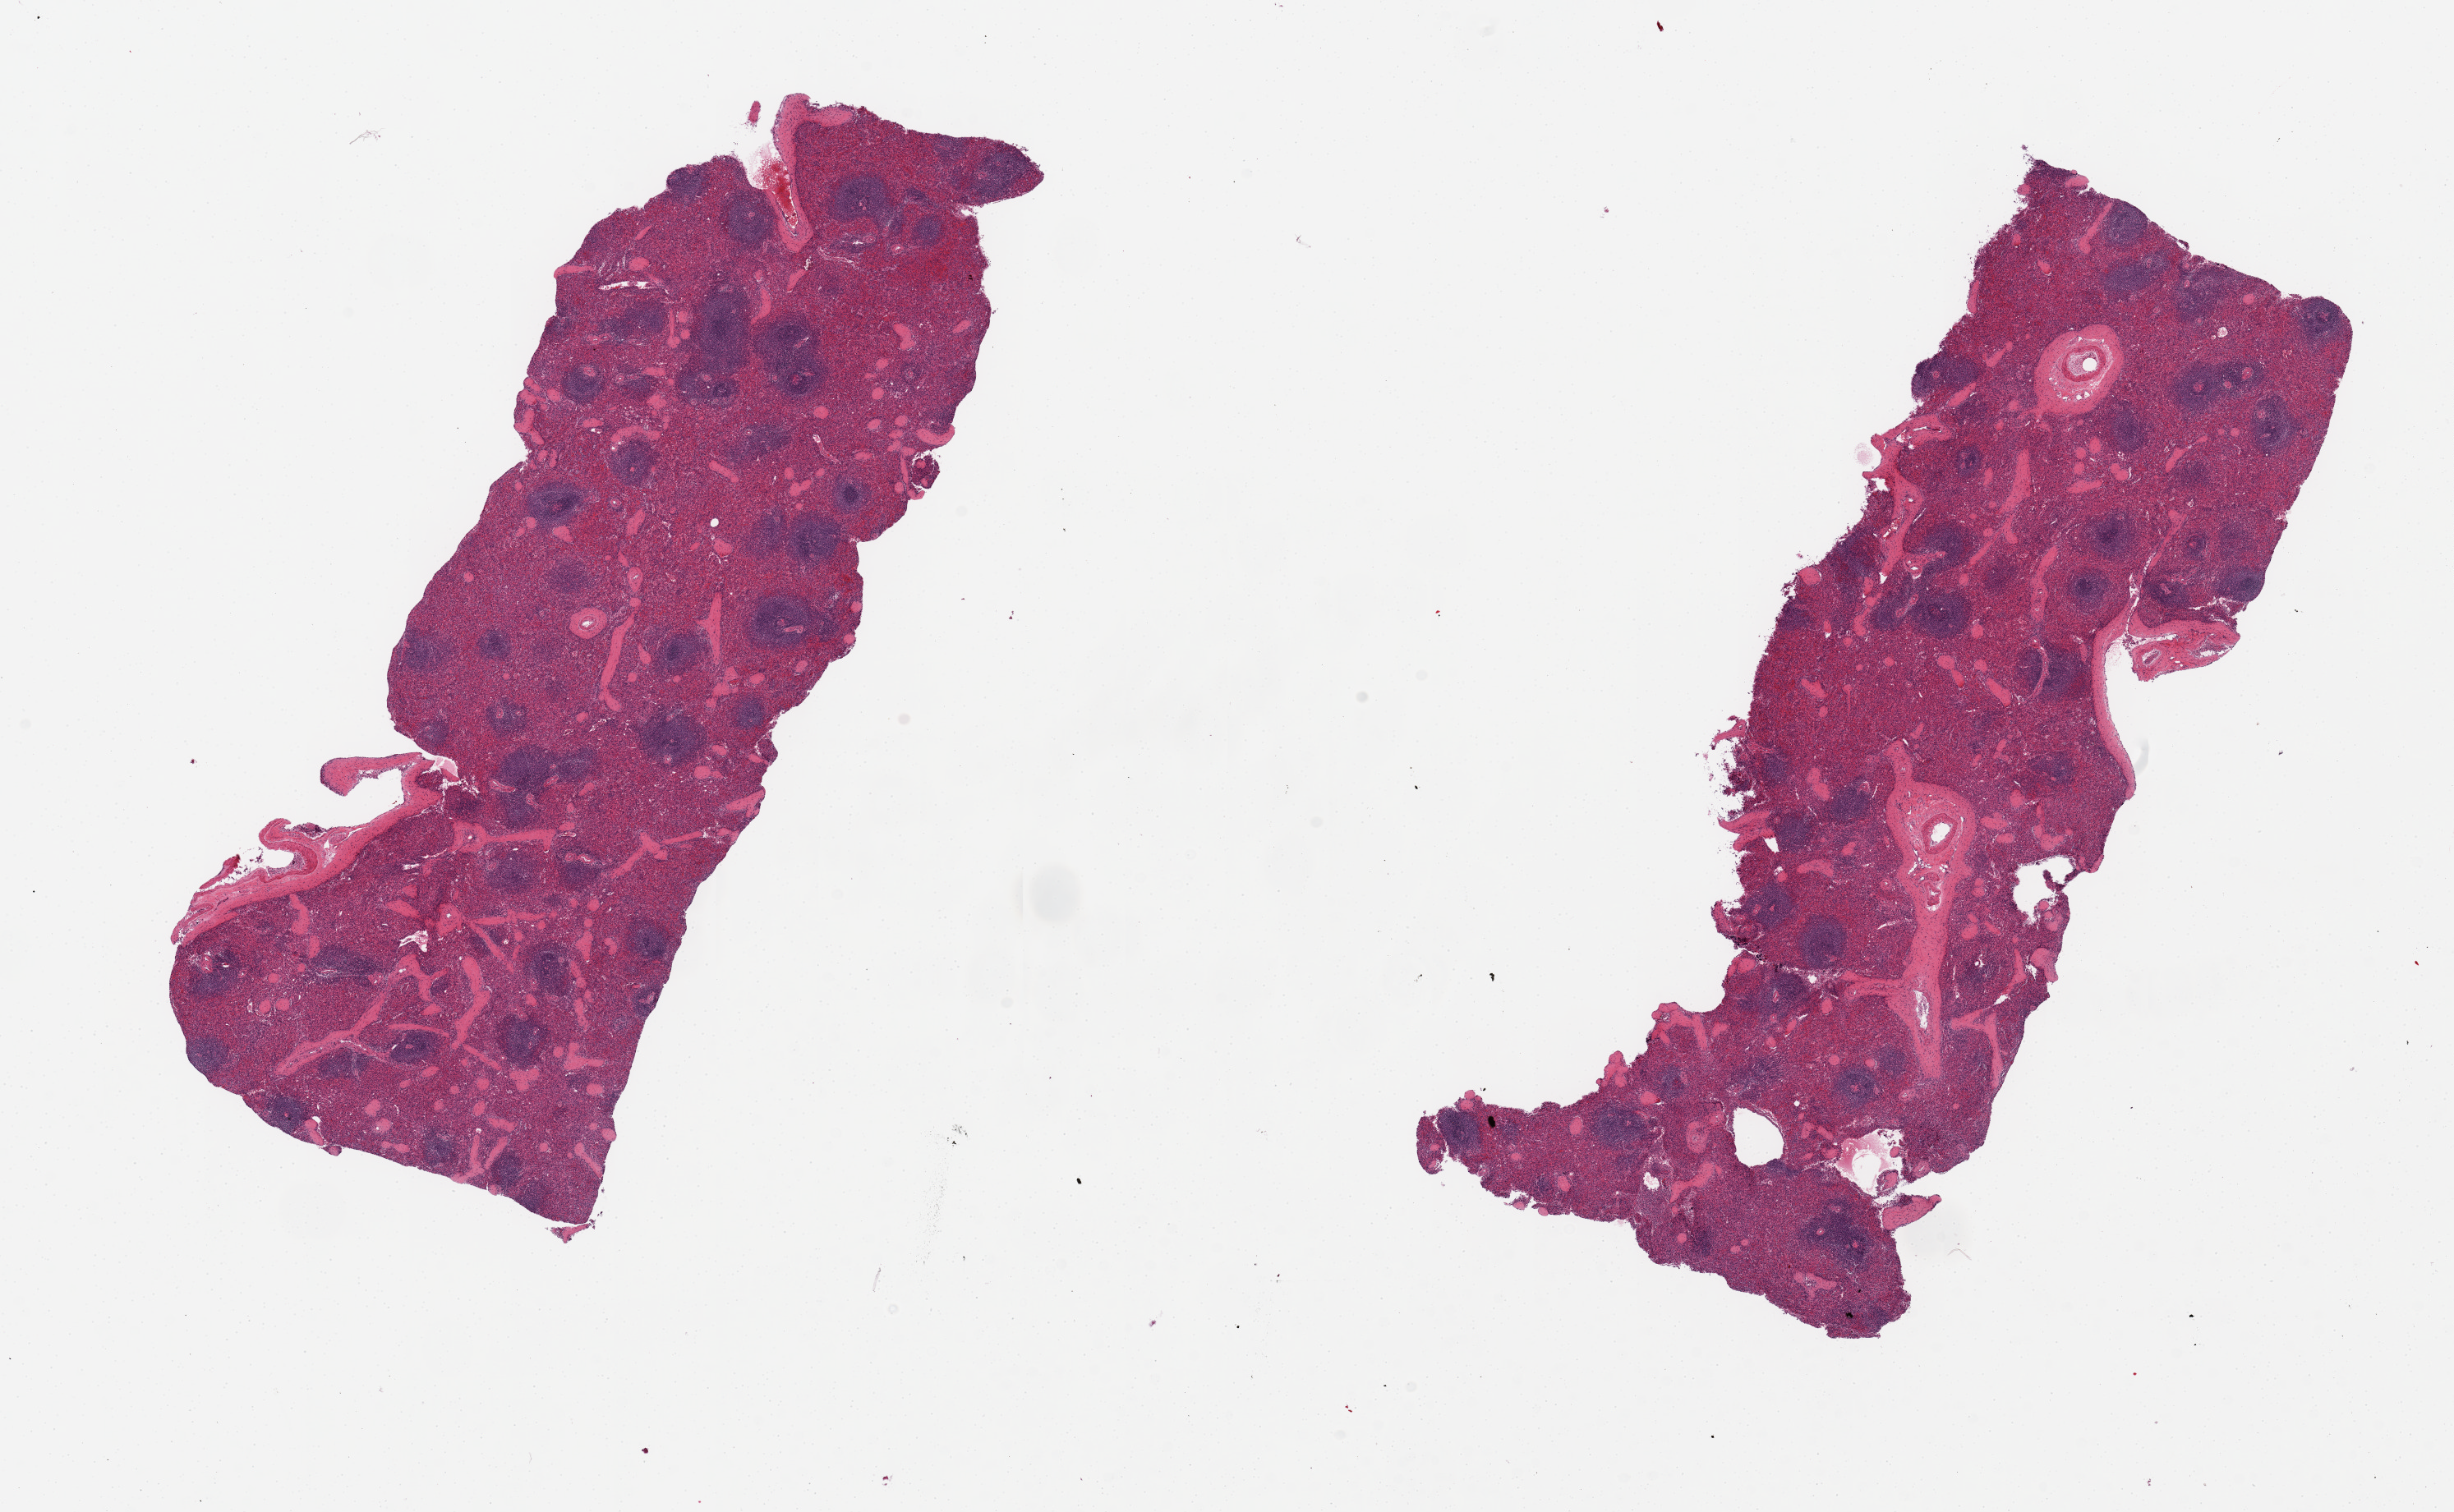
Whole-slide image, hematoxylin and eosin (H&E) stain, brightfield, whole scanned area (about 23.6 x 14.6 mm, slide scanned at 20x) shown as a low-resolution overview; PAXgene-fixed, paraffin-embedded tissue; target tissue: spleen; tissue donor sample. Donor: female.
Reviewer comment on this tissue sample: 2 pieces.